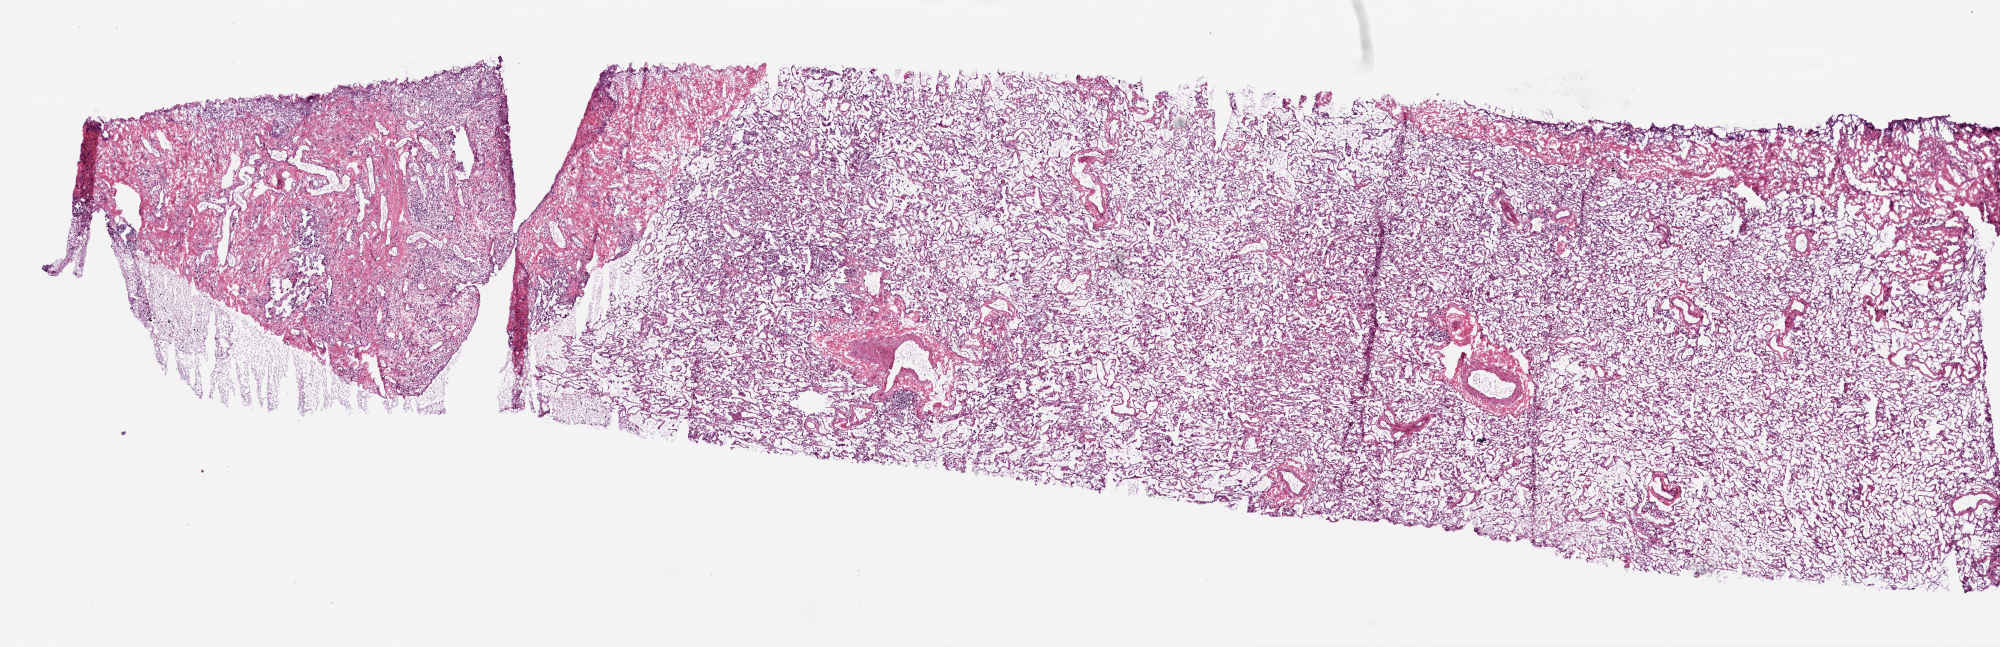
Whole-slide histology image, Hematoxylin and eosin (H&E) stained, low-resolution overview of the scanned area, about 16.0 x 5.2 mm. Frozen section from the top of the tissue portion. Lung, solid tissue normal (non-tumour tissue) sample. Patient: male, age at initial diagnosis 53 years.
This section: solid tissue normal (non-tumour) sample from the same patient. Patient diagnosis: Adenocarcinoma, NOS (lower lobe, lung).